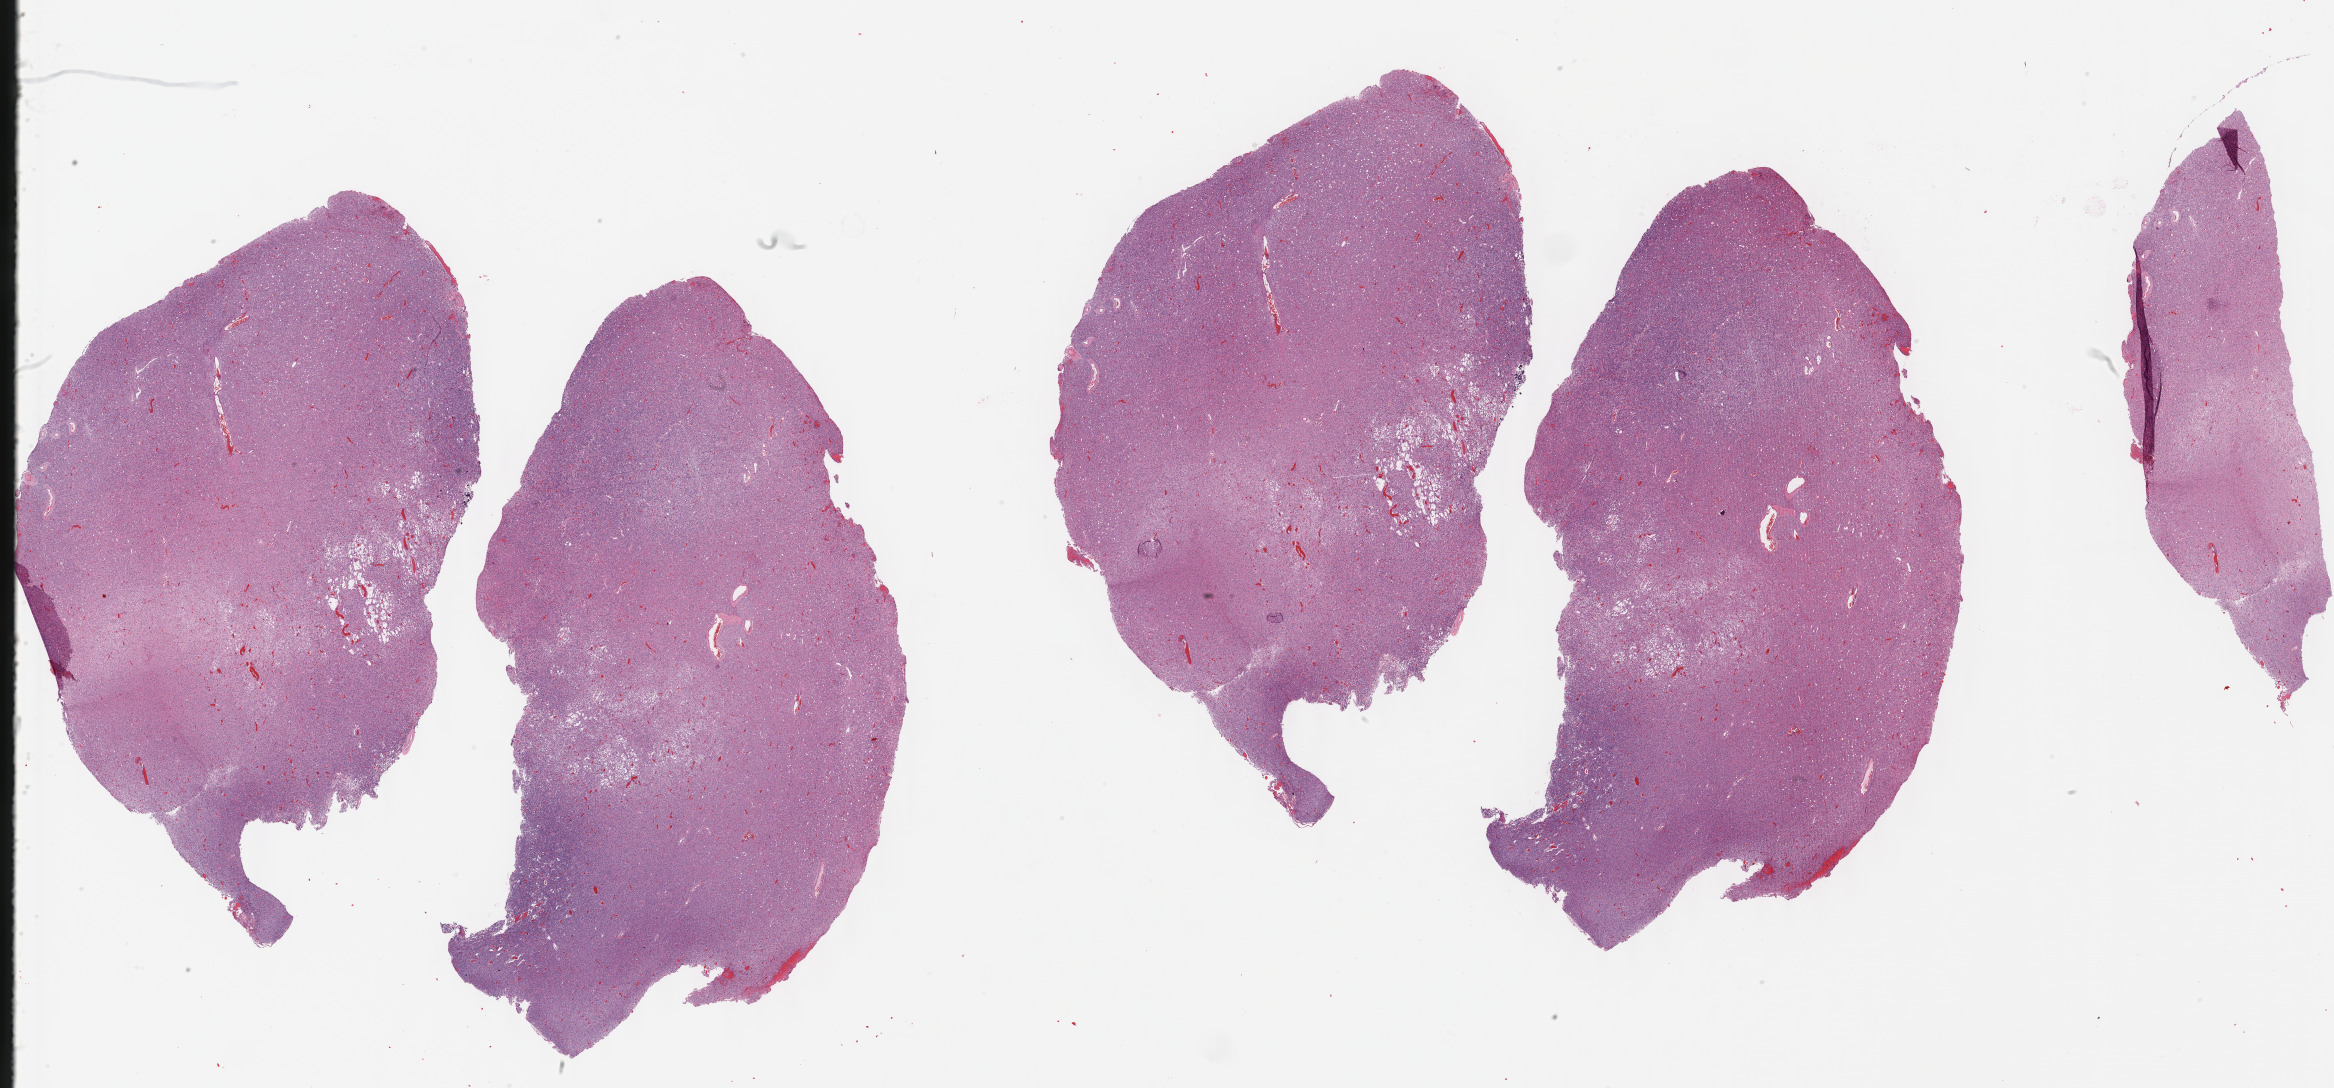
H&E whole-slide image — low-resolution overview of the scanned area, about 37.7 x 17.6 mm (slide scanned at 40x); formalin-fixed paraffin-embedded (FFPE) diagnostic section; brain, primary tumour sample. Patient: female, age at initial diagnosis 30 years. Histologic grade: G2 (moderately differentiated).
- histologic diagnosis: Oligodendroglioma, NOS (cerebrum)
- laterality: right